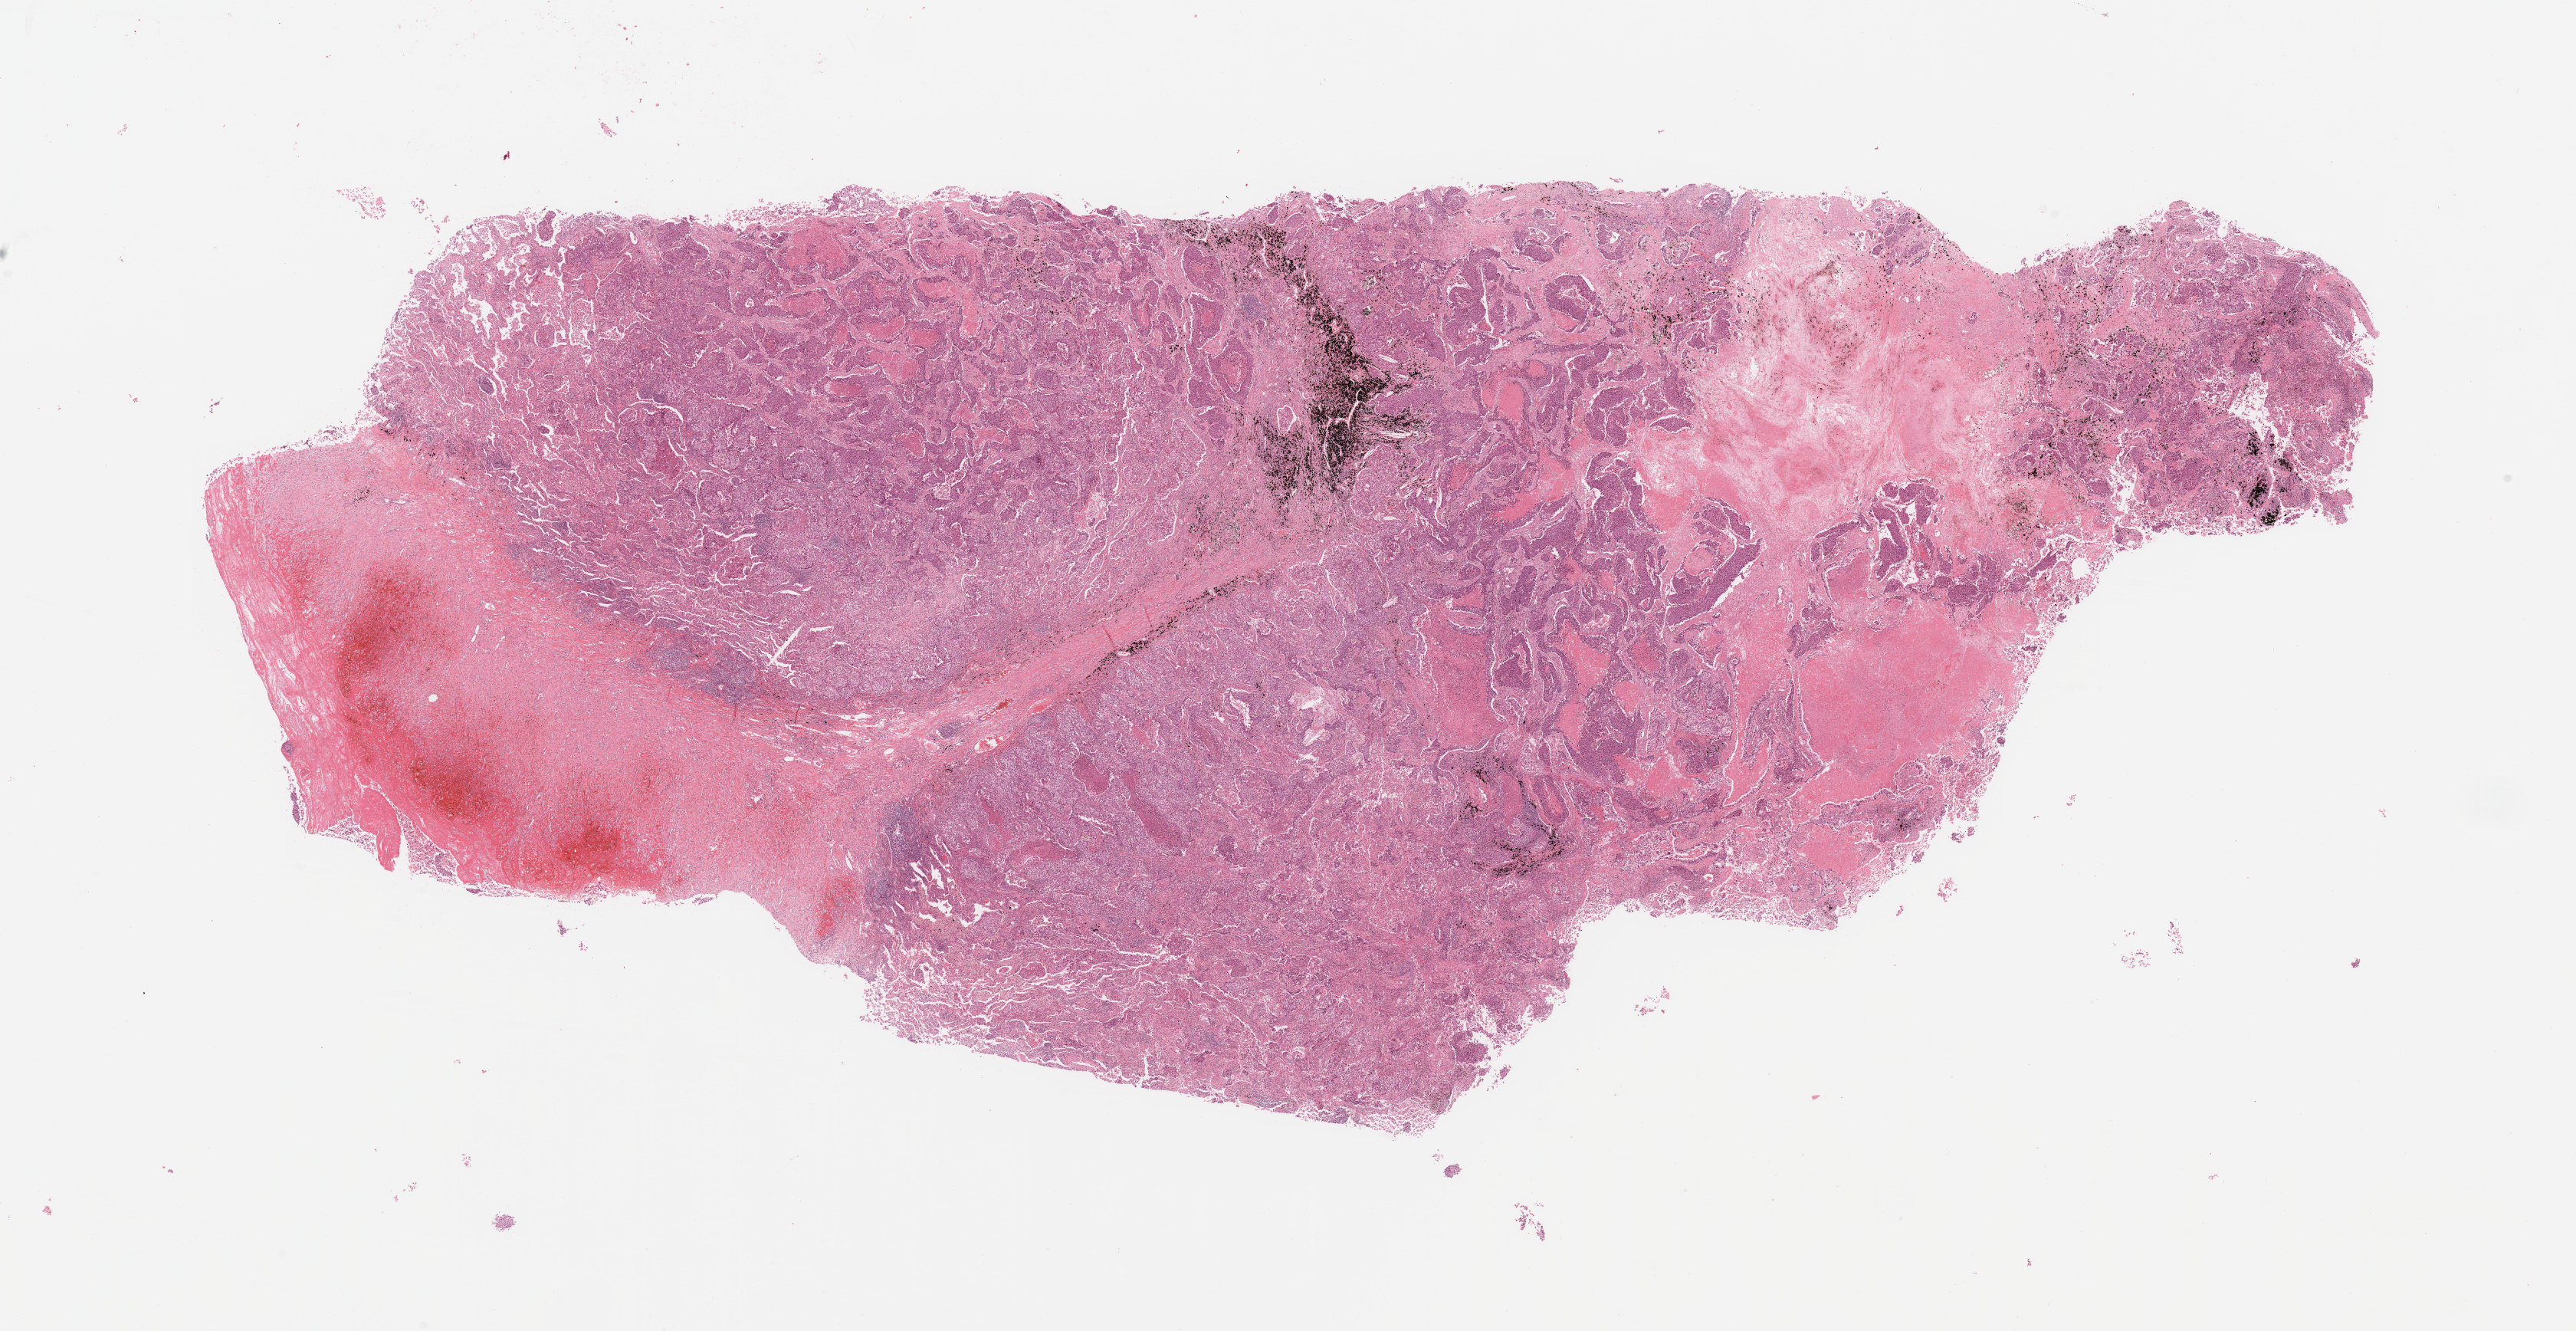
Whole-slide histology image, H&E-stained, low-resolution overview of the scanned area, about 26.6 x 13.7 mm, lung, tumour tissue. Male, 56 y/o. Histologic grade: G3 (poorly differentiated).
AJCC pathologic stage: IB. Primary tumour site (as recorded): left upper lobe. Diagnosis: Adenocarcinoma, NOS.